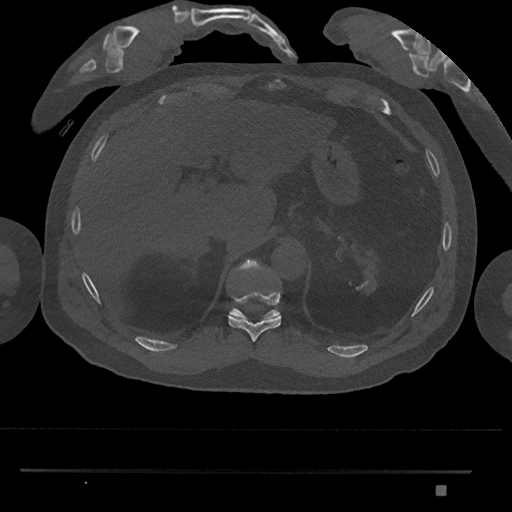
CT including the spine, one axial slice. Slice 986 of 1134 in the series (ordered by position). Reconstruction kernel Br40s/3. 120 kVp. Bone window (W 1800 / L 400 HU). 512 × 512 image matrix, field of view 429 × 429 mm. Patient: male, 65 years. From the clinical record (not read from this slice): primary cancer: prostate.
Structures marked on this image (semi-automatic segmentation, software-assisted and operator-edited):
- T10 vertebra: bounding box <228,291,281,342> (left, top, right, bottom; pixels)
- T11 vertebra: <229,259,280,319>